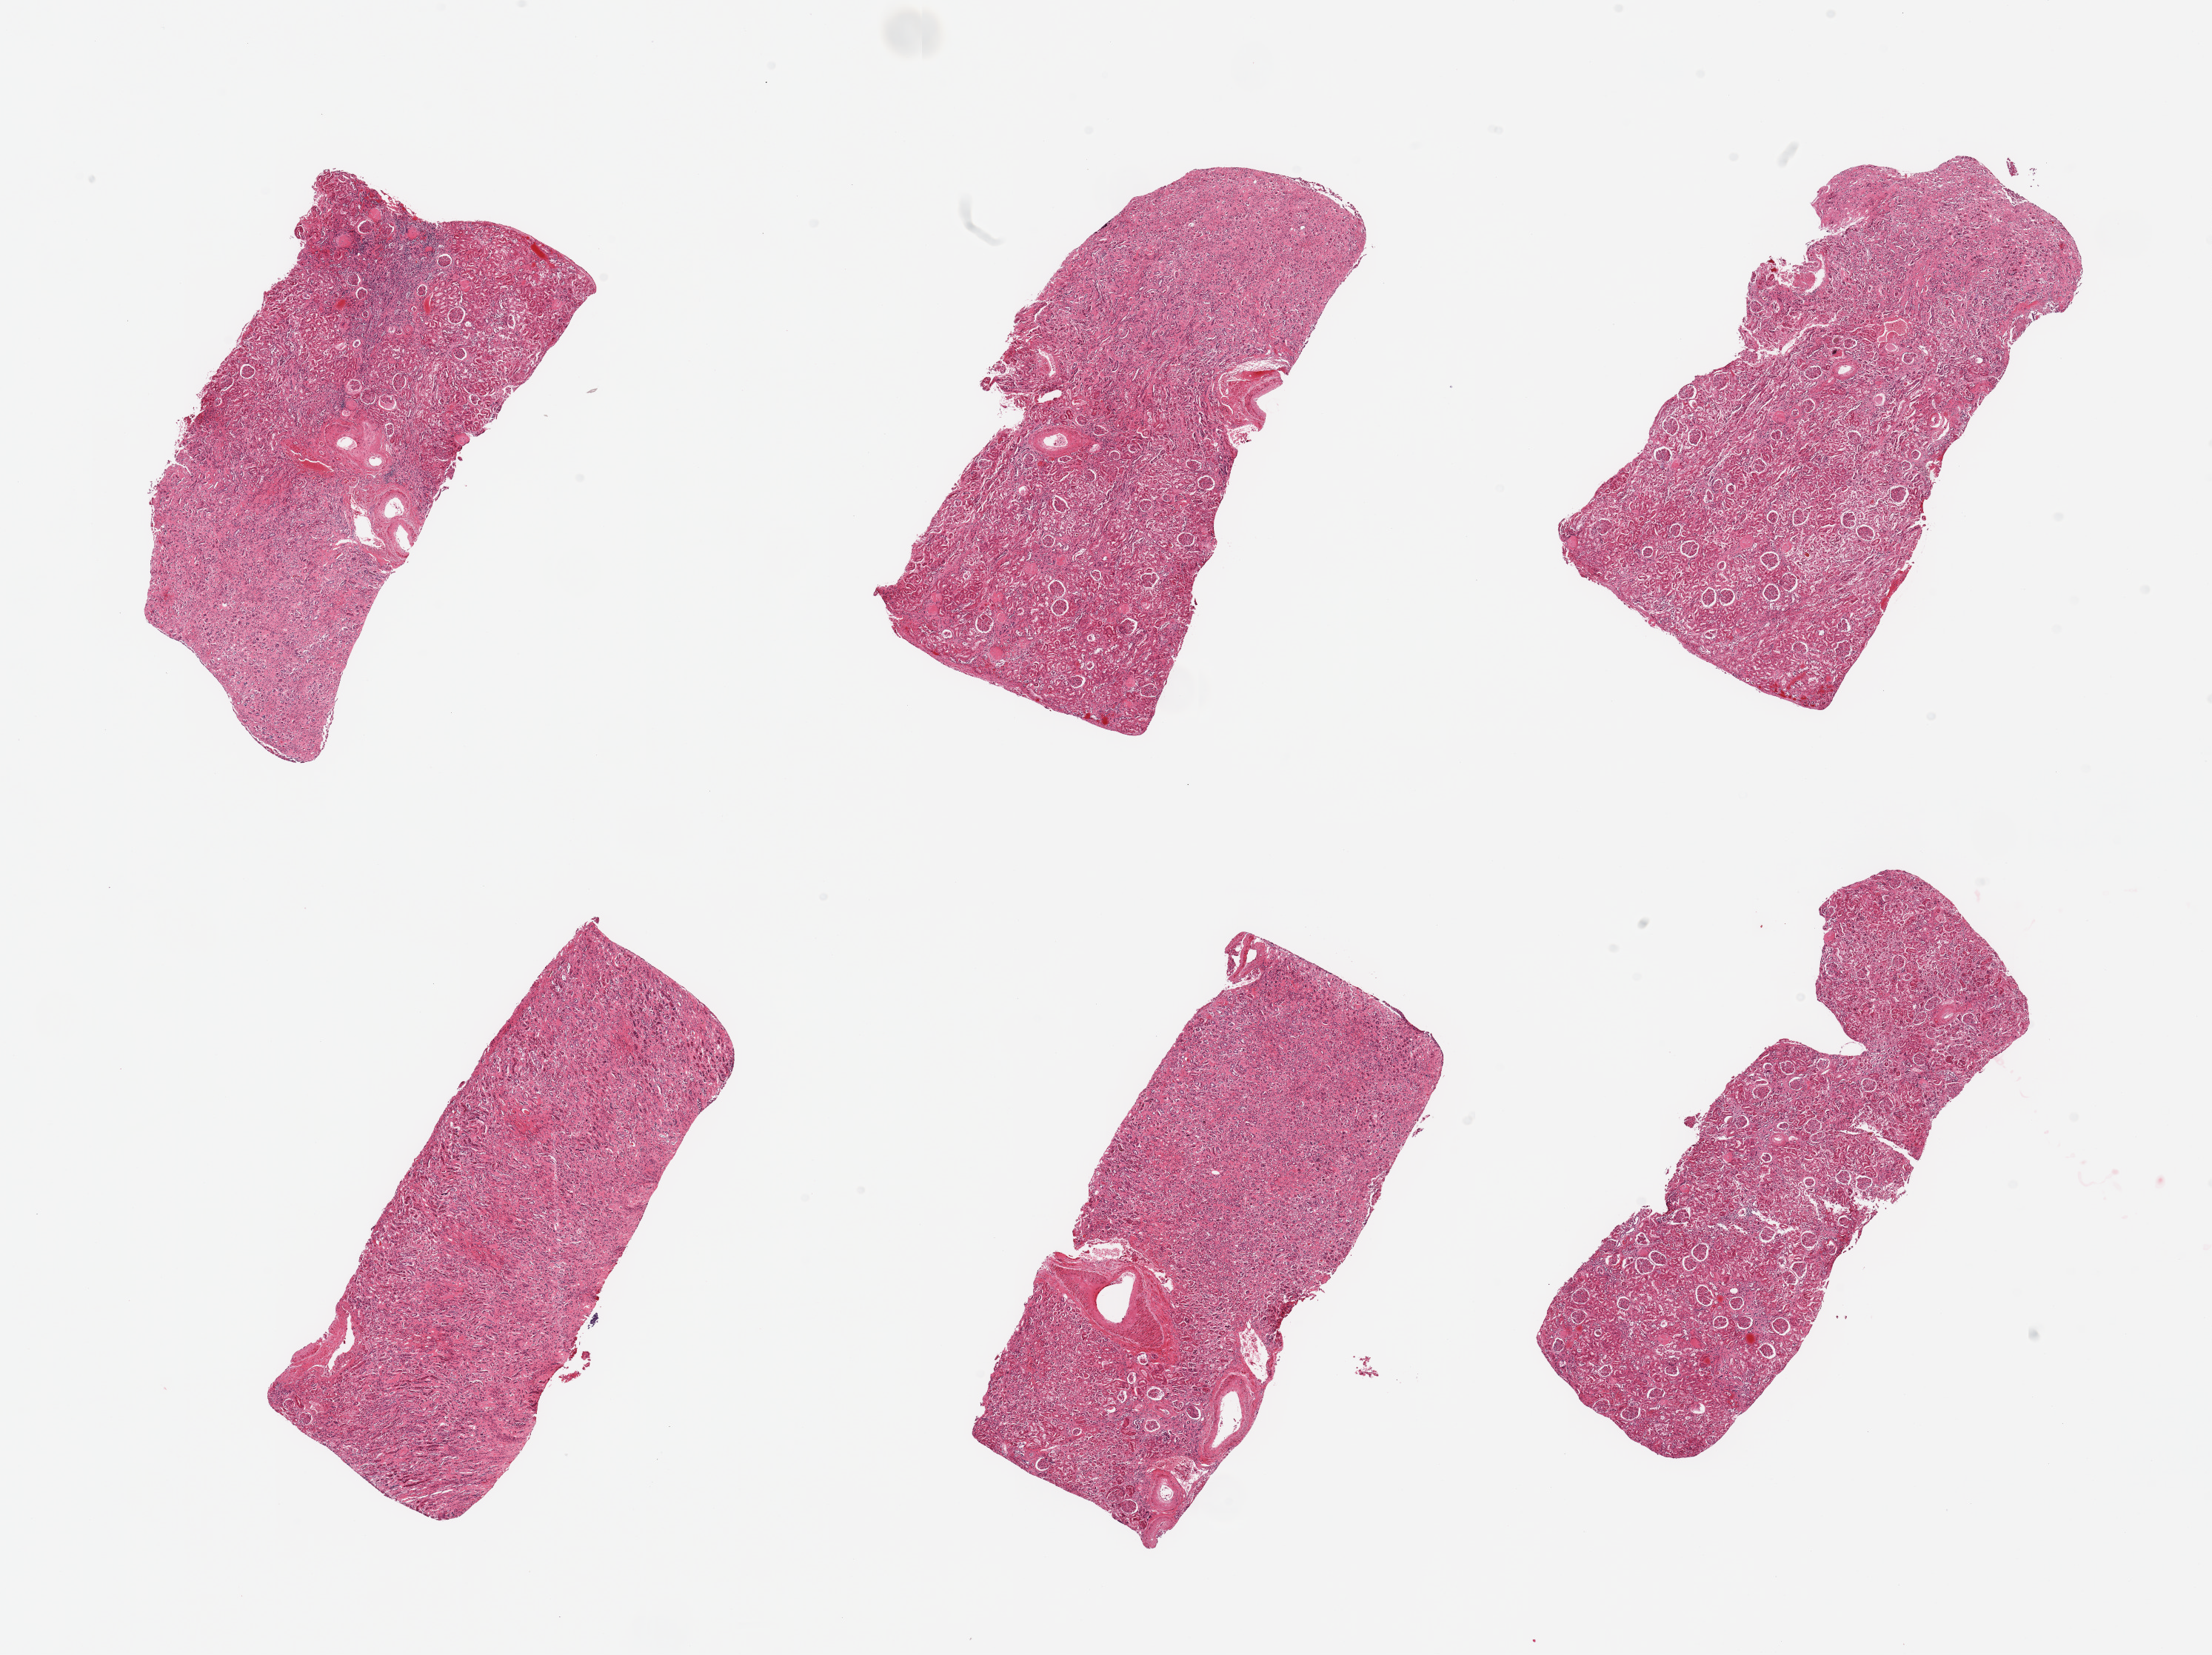
Whole-slide image, haematoxylin and eosin stain, low-resolution overview of the scanned area, about 23.6 x 17.7 mm; PAXgene-fixed paraffin-embedded (PFPE) section; sampled site (target tissue): renal cortex; donor tissue sample.
* pathologist's review note for this sample: 6 pieces, glomeruli present, moderate interstitial fibrosis